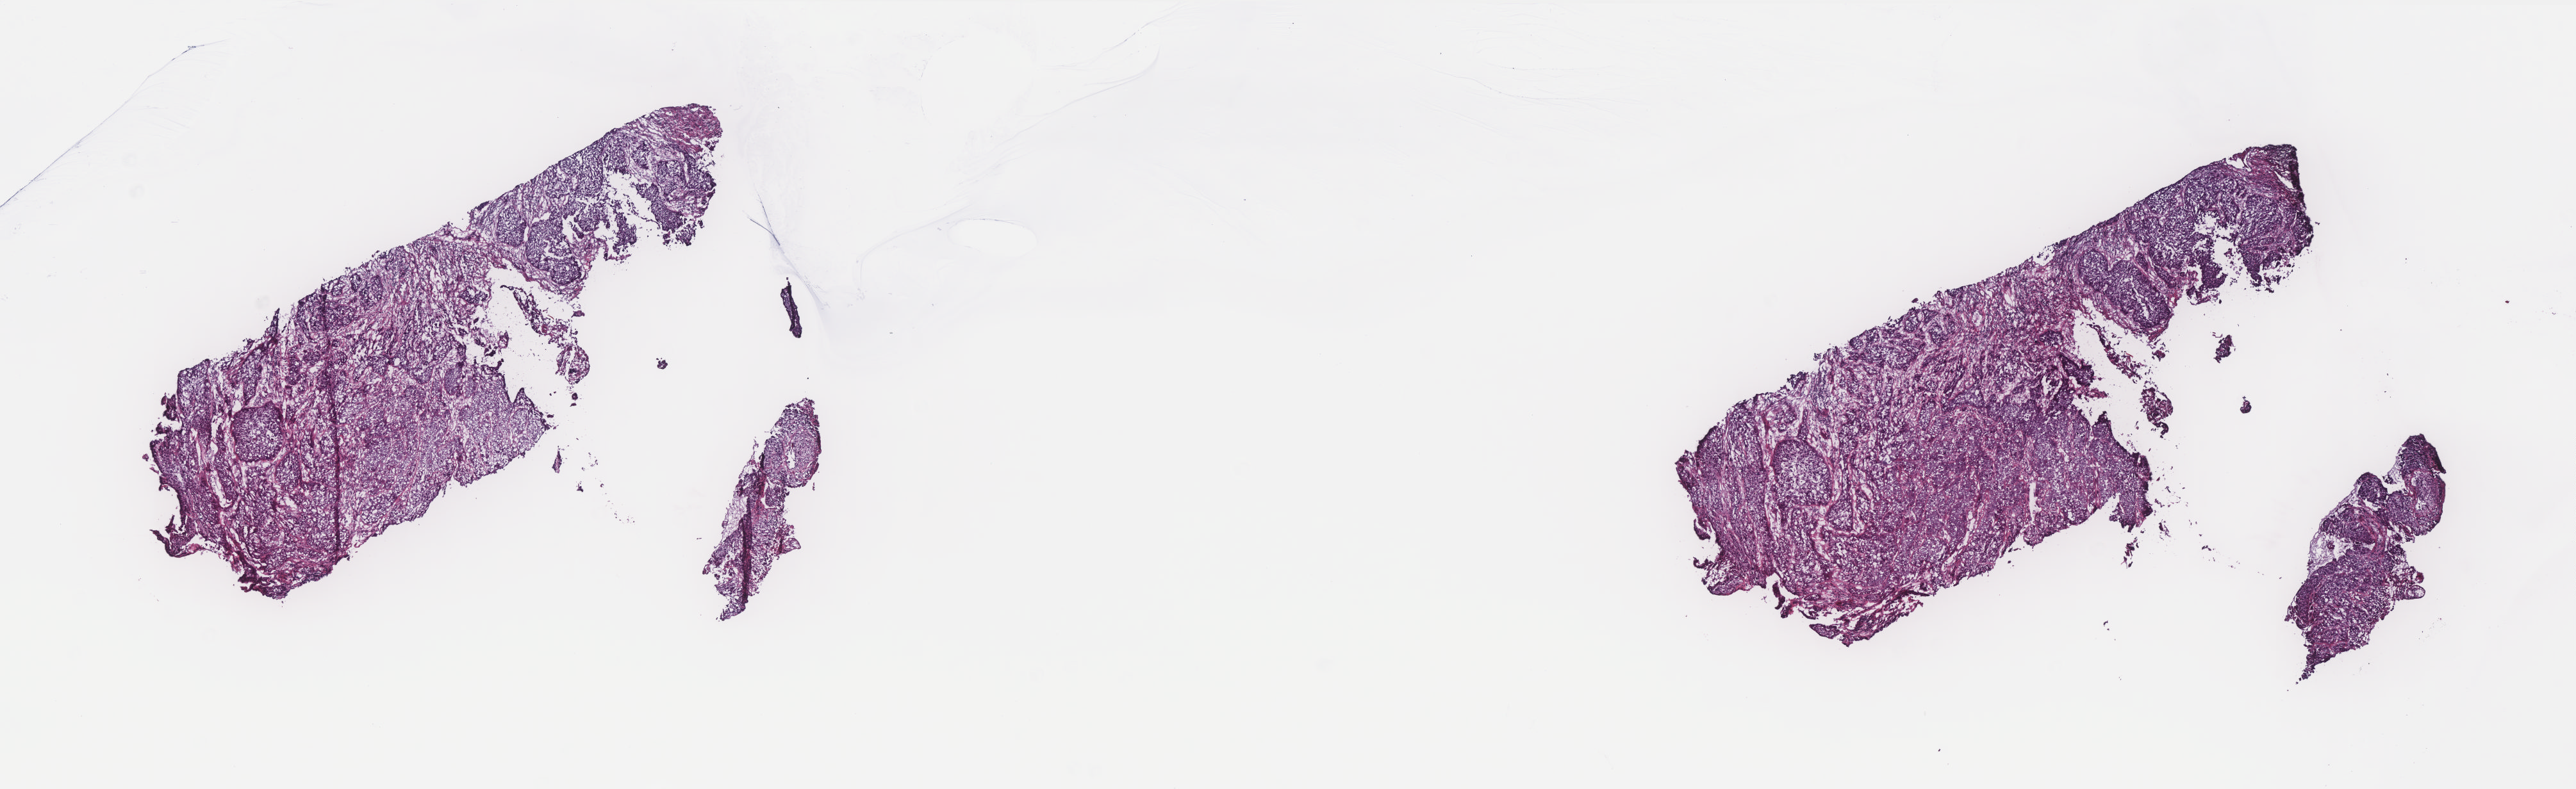
H&E whole-slide image — whole scanned area (about 16.1 x 4.9 mm, from a 40x scan) shown as a low-resolution overview, frozen section from the top of the tissue portion, cervix, primary tumour sample. Female, age 26 years at initial diagnosis. Histologic grade: G3 (poorly differentiated). Pathologist review of this section (percent, as recorded): tumour cells 80%, tumour nuclei 80%, normal cells 0%, stromal cells 20%, necrosis 0%. Infiltration values recorded for this section: lymphocyte infiltration 25%, monocyte infiltration 0%, neutrophil infiltration 8%.
* pathologic diagnosis: Squamous cell carcinoma, NOS (cervix uteri)
* FIGO stage: IB2